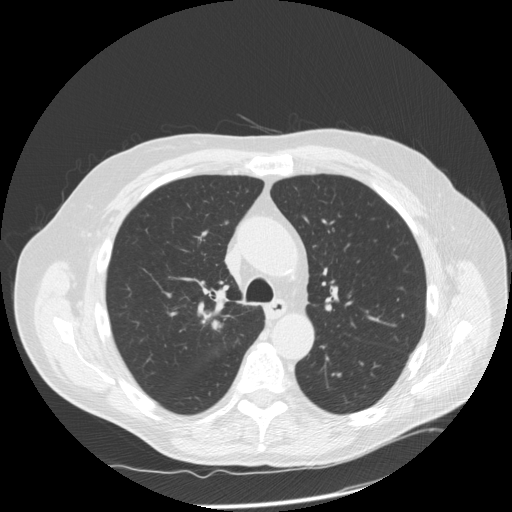
Low-dose screening chest CT, axial slice; third annual screen; lung window (W 1500 / L -600 HU); standard (soft-tissue) reconstruction kernel (STANDARD); slice 55 of 166 in the series; 512 × 512 image matrix. Male participant, aged 69 years at enrolment. Former smoker at enrolment.
Expert-annotated lung lesion, bounding box <184,294,243,346> (left, top, right, bottom; pixels). Reader record for this screening exam (exam-level; its link to the box is not recorded): non-calcified nodule or mass ≥4 mm, right upper lobe, 18 × 17 mm, spiculated (stellate) margins, soft tissue attenuation, pre-existing on the prior screen: no. Later outcome: lung cancer diagnosed 13 days after this screen — squamous cell carcinoma, NOS, right upper lobe, poorly differentiated (G3), stage IA (AJCC 6th edition), 22 mm at pathology.